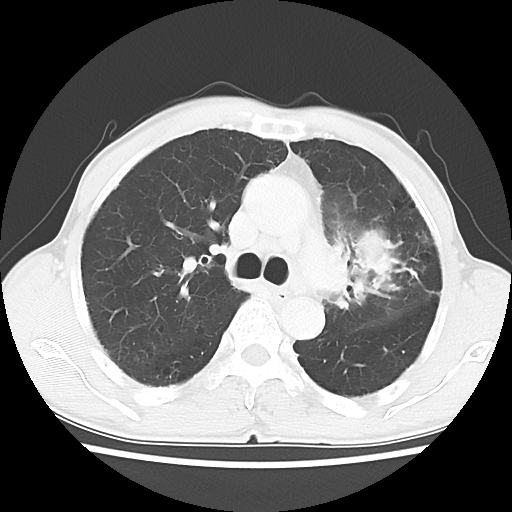
Chest CT, one axial slice; reconstruction kernel LUNG; 120 kVp; lung window (W 1500 / L -600 HU); 5 mm slice thickness; 512 × 512 image matrix. Patient: male, 64 years. From the clinical record (not read from this slice): clinical TNM (as recorded): T3 N3 M0; histopathological grade: G3.
Outlined on this slice (rectangle marked by the reading radiologist):
- lung tumour (recorded histology: adenocarcinoma): bounding box (x1, y1, x2, y2) in pixels: (339, 211, 398, 312)